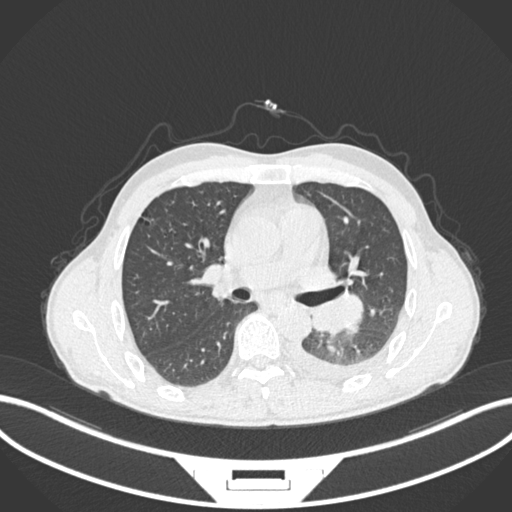
Chest CT, one axial slice. Position 143 of 222 along the scan axis. Reconstruction kernel B30f. 120 kVp. Lung window (W 1500 / L -600 HU). 512 × 512 image matrix. Male patient, age 47 years. Case-level facts recorded for this patient, not image findings: clinical TNM (as recorded): T3 N1 M1c.
Structures marked on this image (rectangle marked by the reading radiologist):
- lung tumour (recorded histology: small cell carcinoma): bounding box [x1, y1, x2, y2] px = [307, 291, 369, 338]